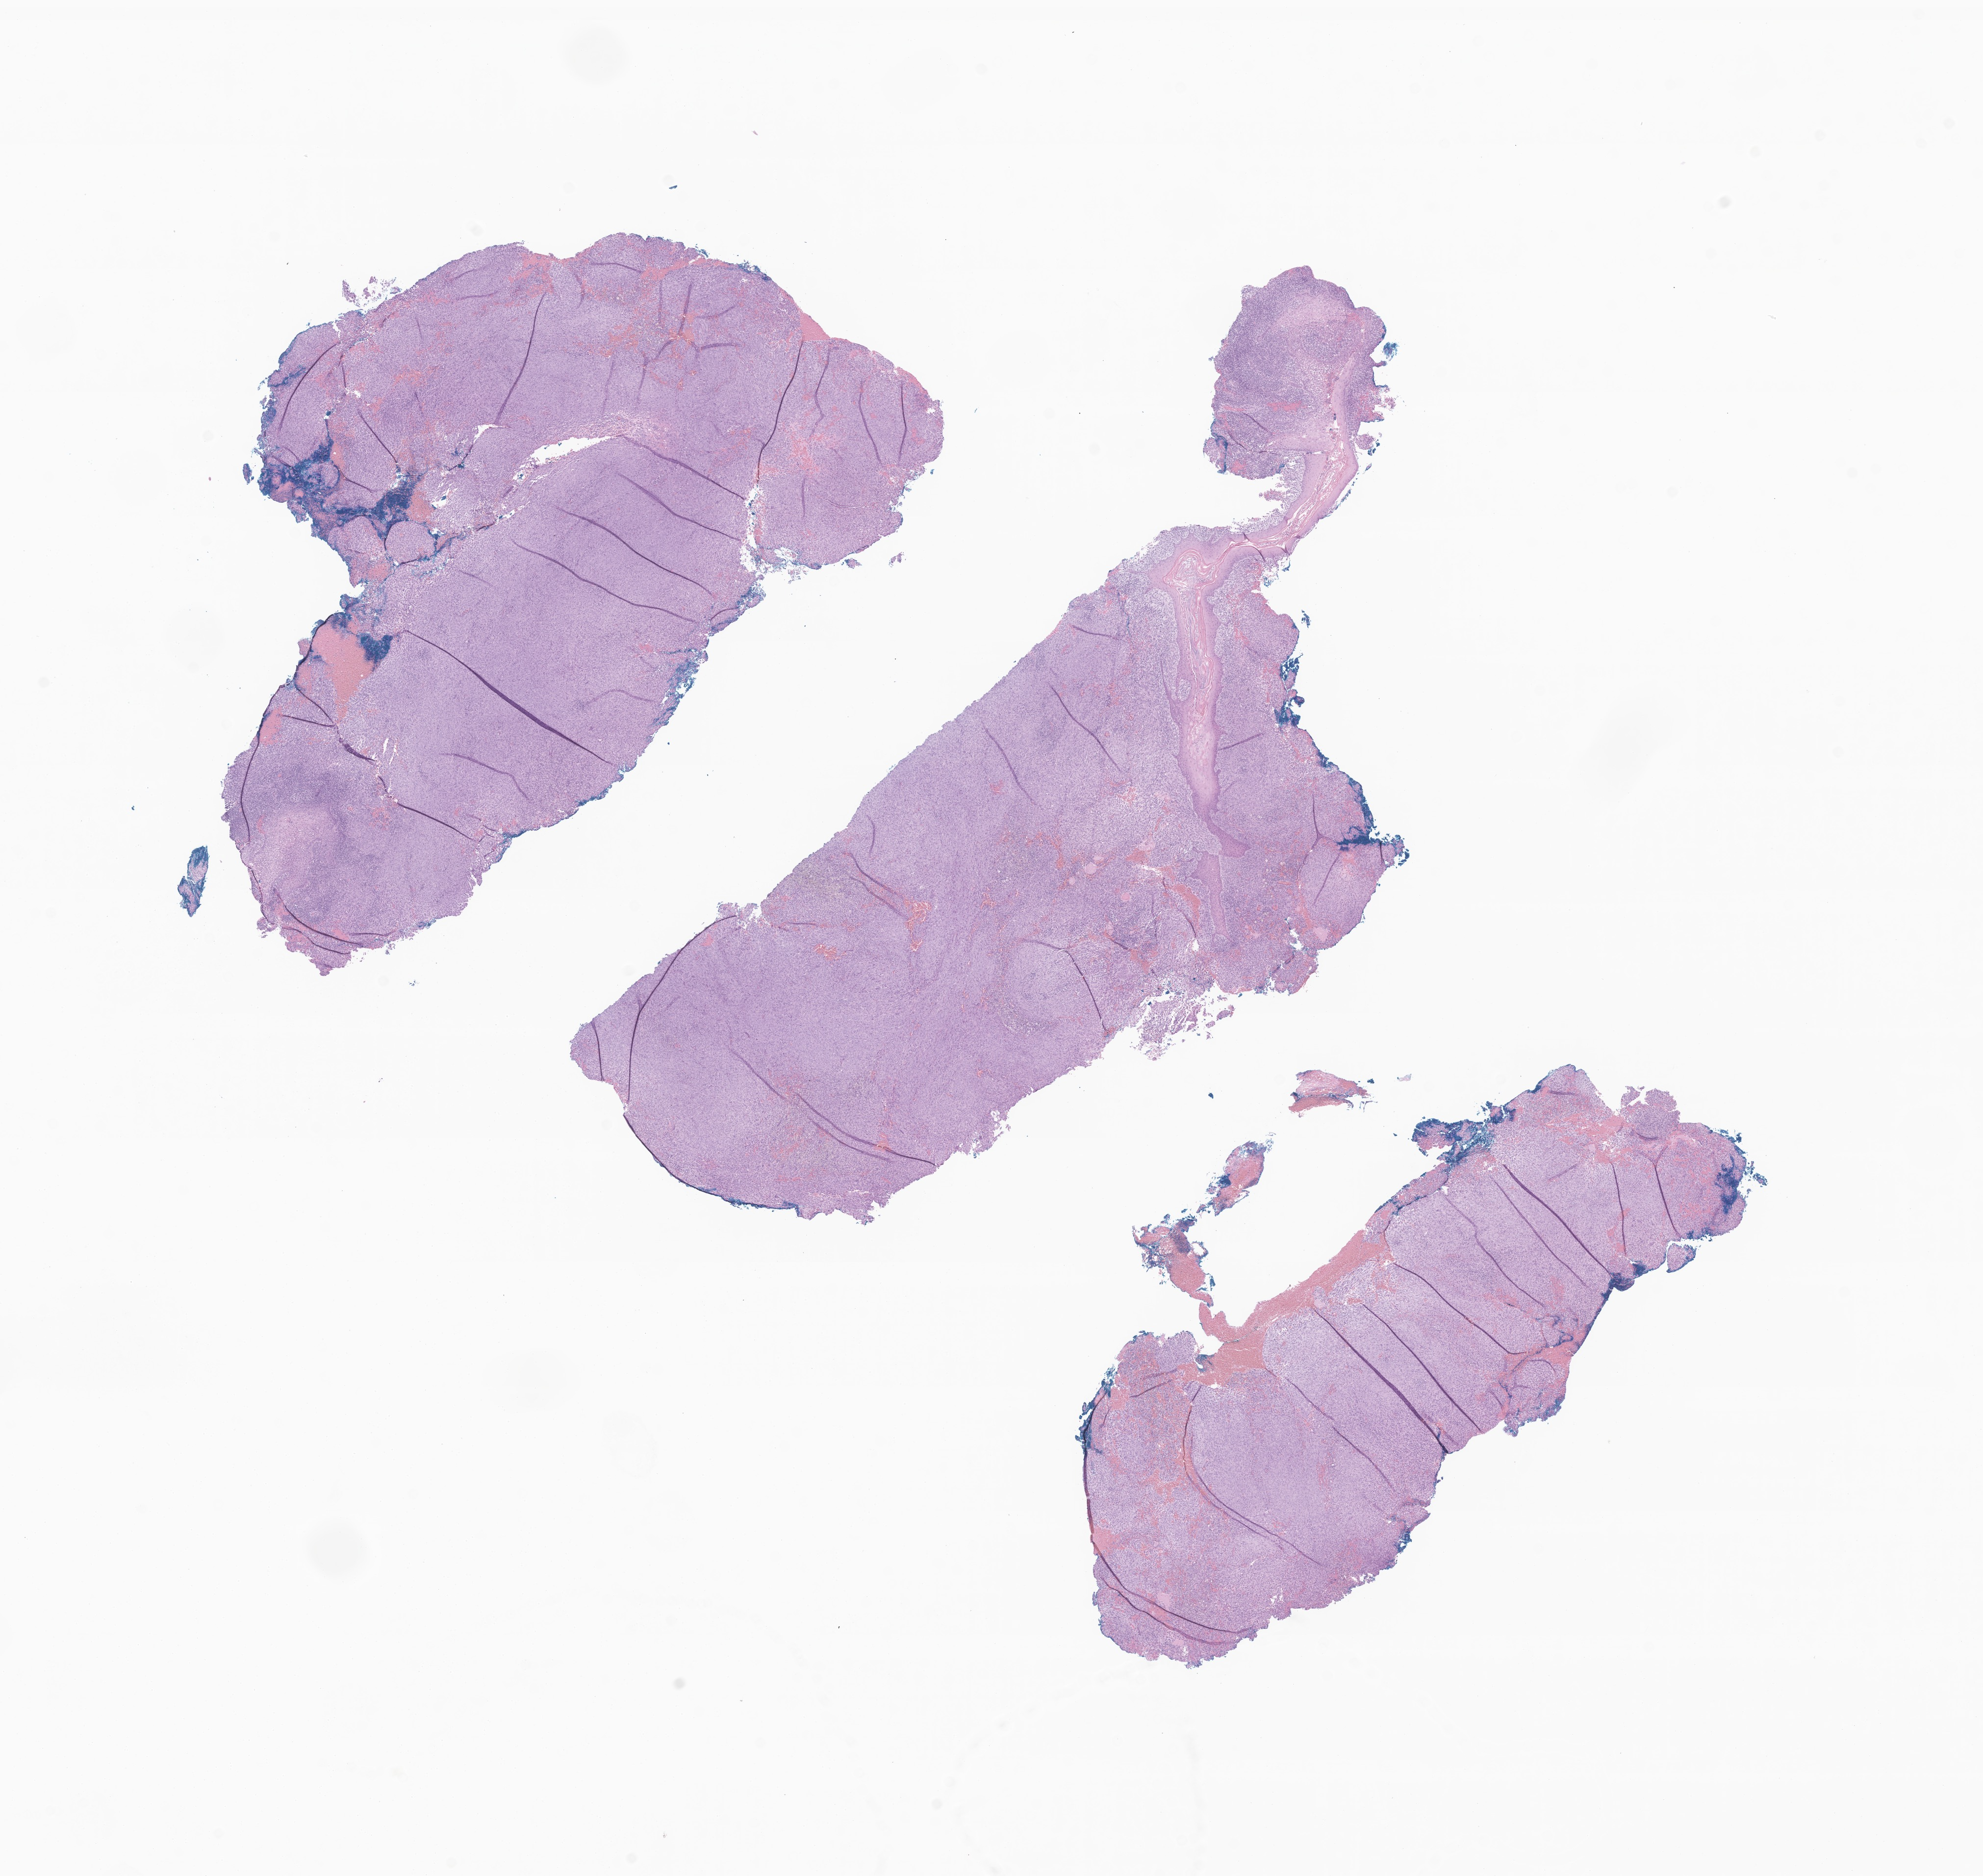
Haematoxylin and eosin whole-slide image of tumor tissue from the mandible — shown as a low-resolution overview of the whole scanned area (about 17.0 x 16.1 mm); FFPE section. Female patient, age 180 months (15 years).
- diagnosis (ICD-O-3 morphology term): Myofibroblastic tumor, NOS